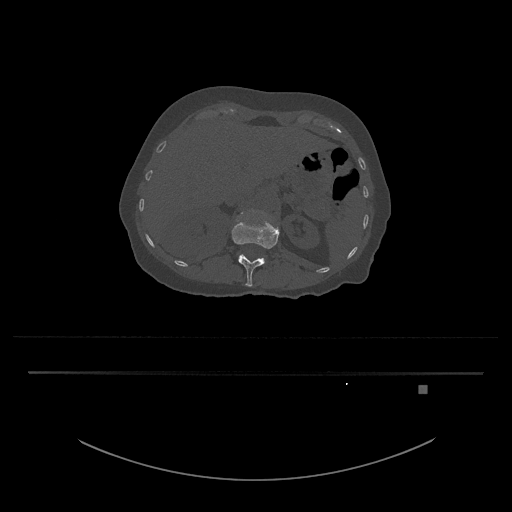
CT including the spine, one axial slice; slice 541 of 797 in the series (ordered by position); reconstruction kernel Br40s/3; 120 kVp; bone window (W 1800 / L 400 HU); 512 × 512 image matrix, field of view 500 × 500 mm. Female patient, age 57 years. From the clinical record (not read from this slice): primary cancer: cervical.
Structures marked on this image (semi-automatic segmentation, software-assisted and operator-edited):
- L1 vertebra: bounding box [x1, y1, x2, y2] px = [231, 217, 280, 287]